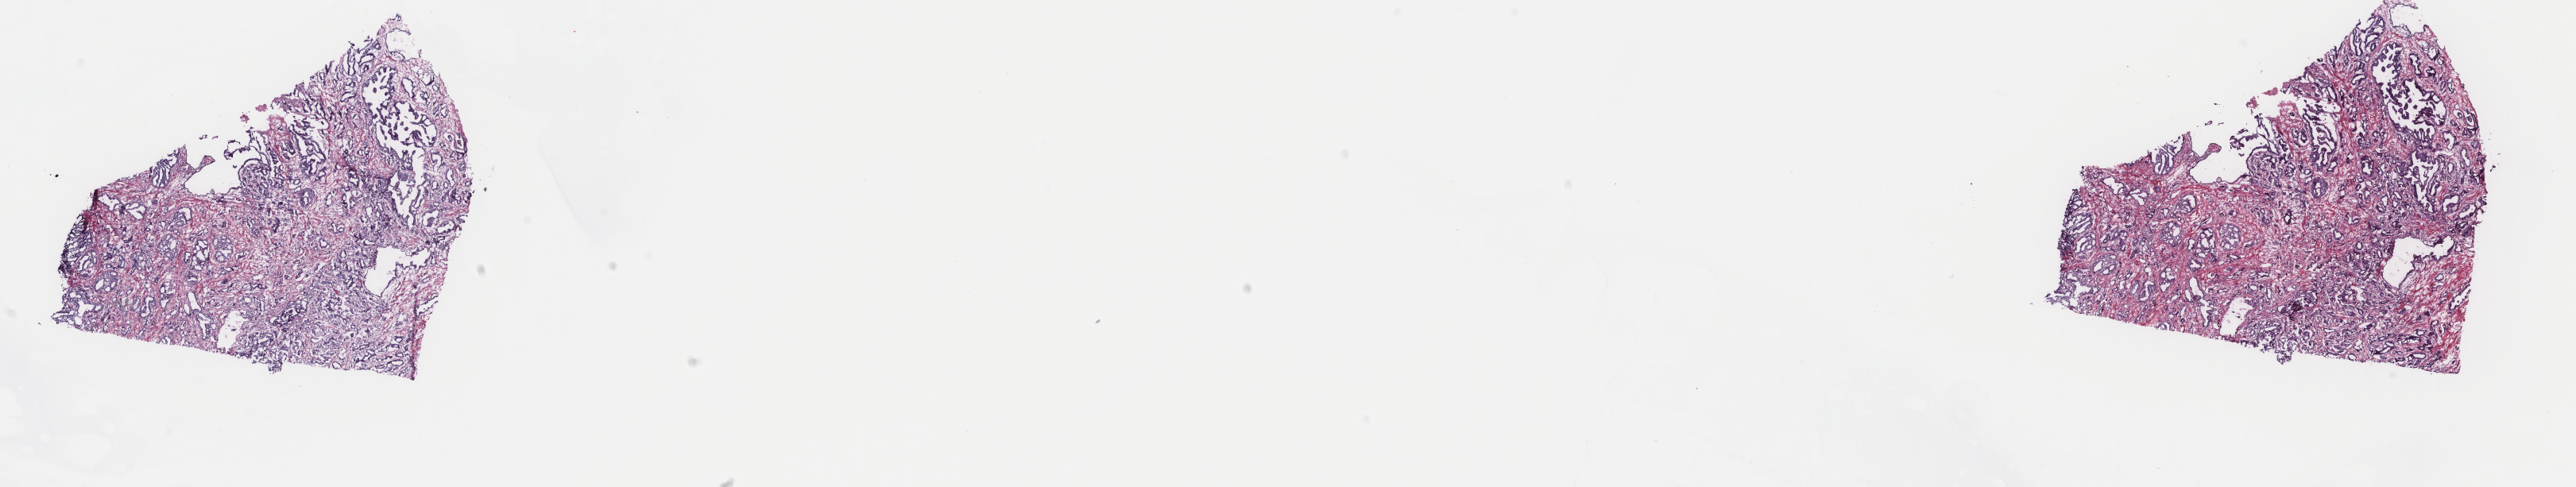
Digitized Hematoxylin and eosin (H&E) stained tissue section (whole slide), whole scanned area (about 25.7 x 4.9 mm, acquisition: 40x scan) shown as a low-resolution overview. Frozen section. Prostate, primary tumour sample. Patient: male, age at initial diagnosis 56 years. Gleason score: 7 (4+3). Slide review estimates, as recorded: tumour cells 70%, tumour nuclei 70%, normal cells 0%, stromal cells 30%, necrosis 0%. Infiltration values recorded for this section: lymphocyte infiltration 40%, monocyte infiltration 20%, neutrophil infiltration 20%.
• histologic diagnosis: Adenocarcinoma, NOS (prostate gland)
• lymph nodes positive (case pathology): 0 of 14 examined
• laterality: right